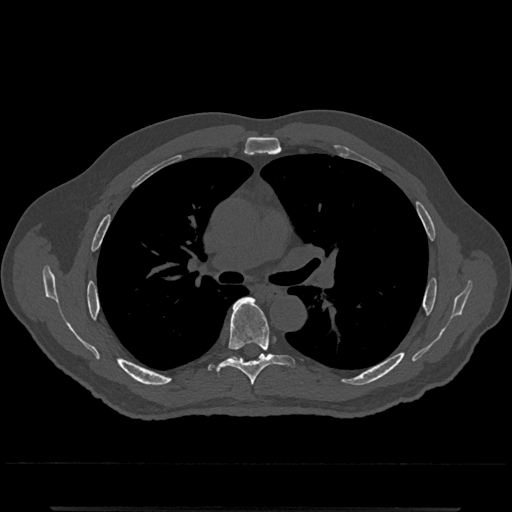
CT including the spine, one axial slice; slice 772 of 797 in the series (ordered by position); reconstruction kernel Br40s/3; bone window (W 1800 / L 400 HU); 0.5 mm slice thickness; 512 × 512 image matrix, field of view 393 × 393 mm. Male patient, age 67 years. Case-level facts recorded for this patient, not image findings: primary cancer: prostate.
Annotated regions visible in this slice (semi-automatically segmented with operator editing):
- T6 vertebra: bounding box (x1, y1, x2, y2) in pixels: (223, 297, 294, 386)